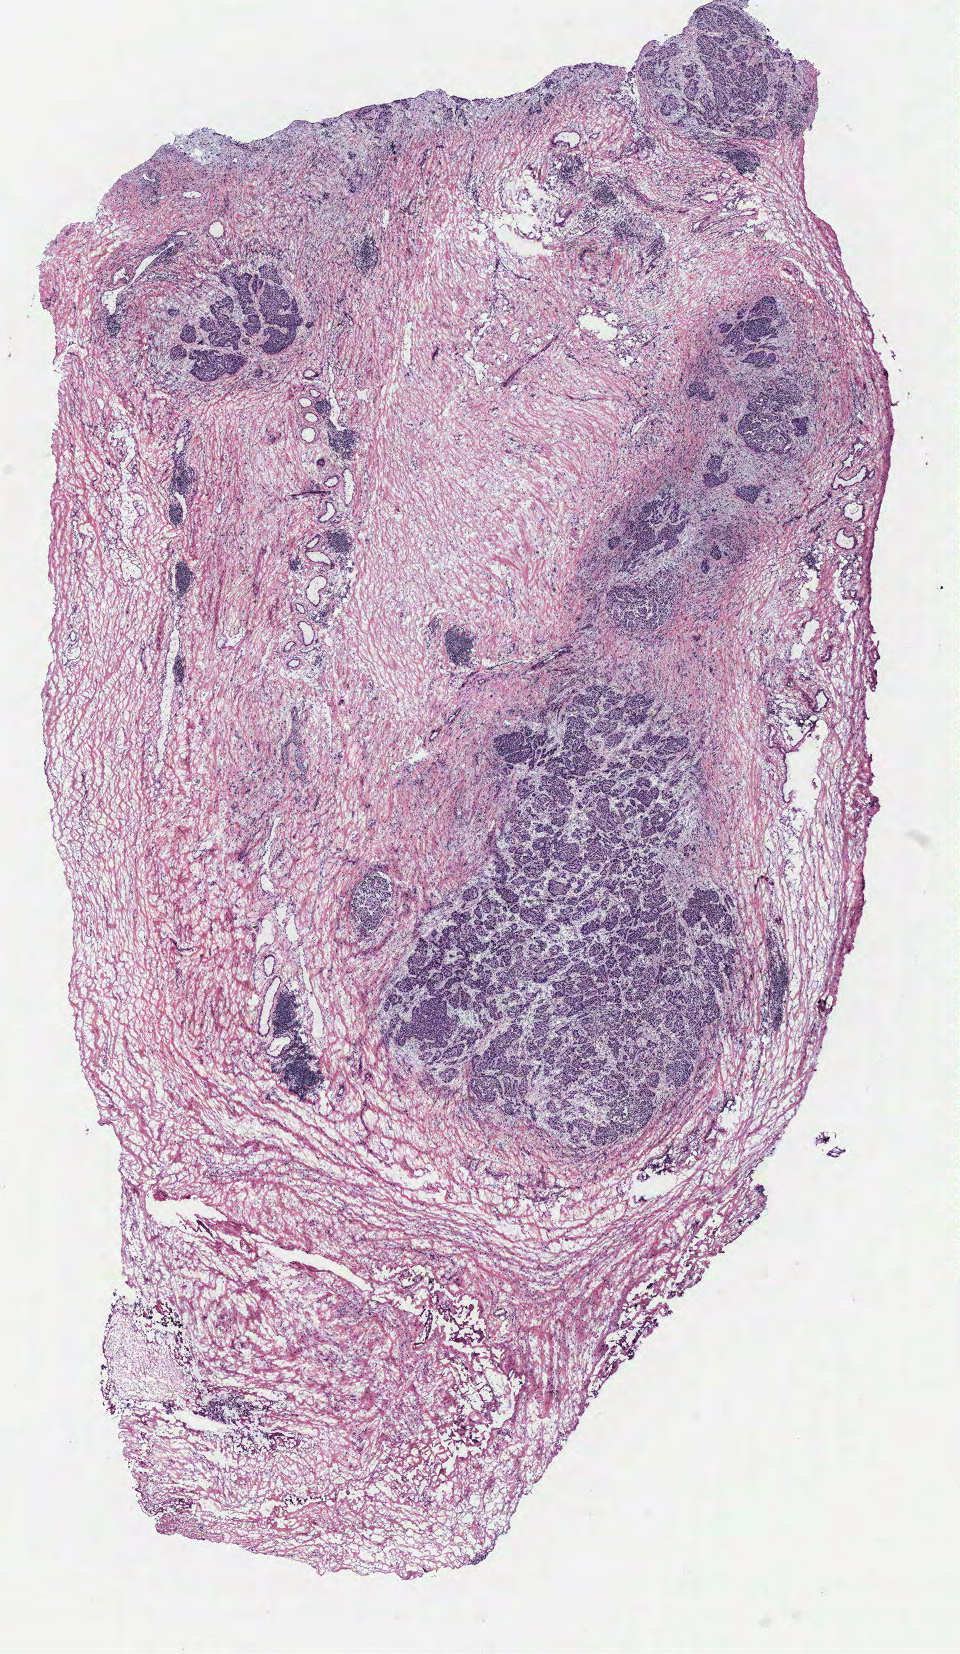
Whole-slide histology image, H&E — low-resolution overview of the scanned area, about 7.7 x 13.2 mm (from a 40x scan), ovary, tumour tissue. 69-year-old female patient.
Primary tumour site (as recorded): ovary. Diagnosis: Serous adenocarcinoma, NOS.